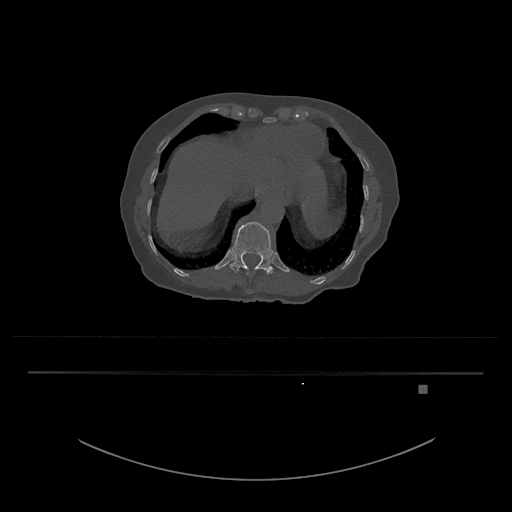
CT including the spine, one axial slice. Position 626 of 797 along the scan axis. Reconstruction kernel Br40s/3. Bone window (W 1800 / L 400 HU). 0.5 mm slice thickness. 512 × 512 image matrix. Patient: female, 57 years. From the clinical record (not read from this slice): primary cancer: cervical.
Structures marked on this image (semi-automatically segmented with operator editing):
- T12 vertebra: bounding box <229,222,274,274> (left, top, right, bottom; pixels)